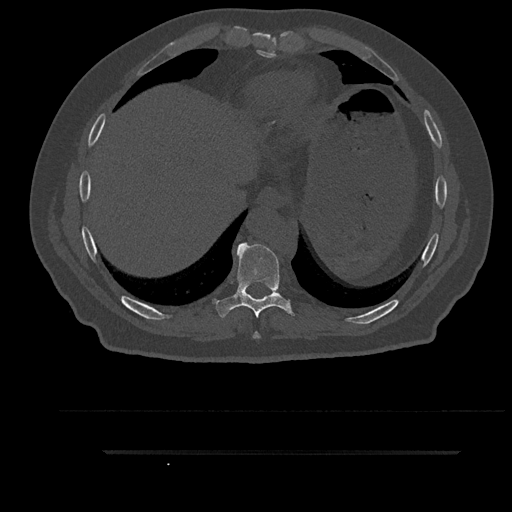
CT including the spine, one axial slice; slice 425 of 797 in the series (ordered by position); 120 kVp; bone window (W 1800 / L 400 HU); 0.5 mm slice thickness; 512 × 512 image matrix, field of view 432 × 432 mm. Patient: male, 63 years. From the clinical record (not read from this slice): primary cancer: renal; vertebrae with lytic lesions (as recorded): T8.
Structures marked on this image (semi-automatic segmentation, software-assisted and operator-edited):
- T8 vertebra: box from (x=253, y=332) to (x=261, y=339) px
- T9 vertebra: (x=214, y=242)–(x=295, y=318)